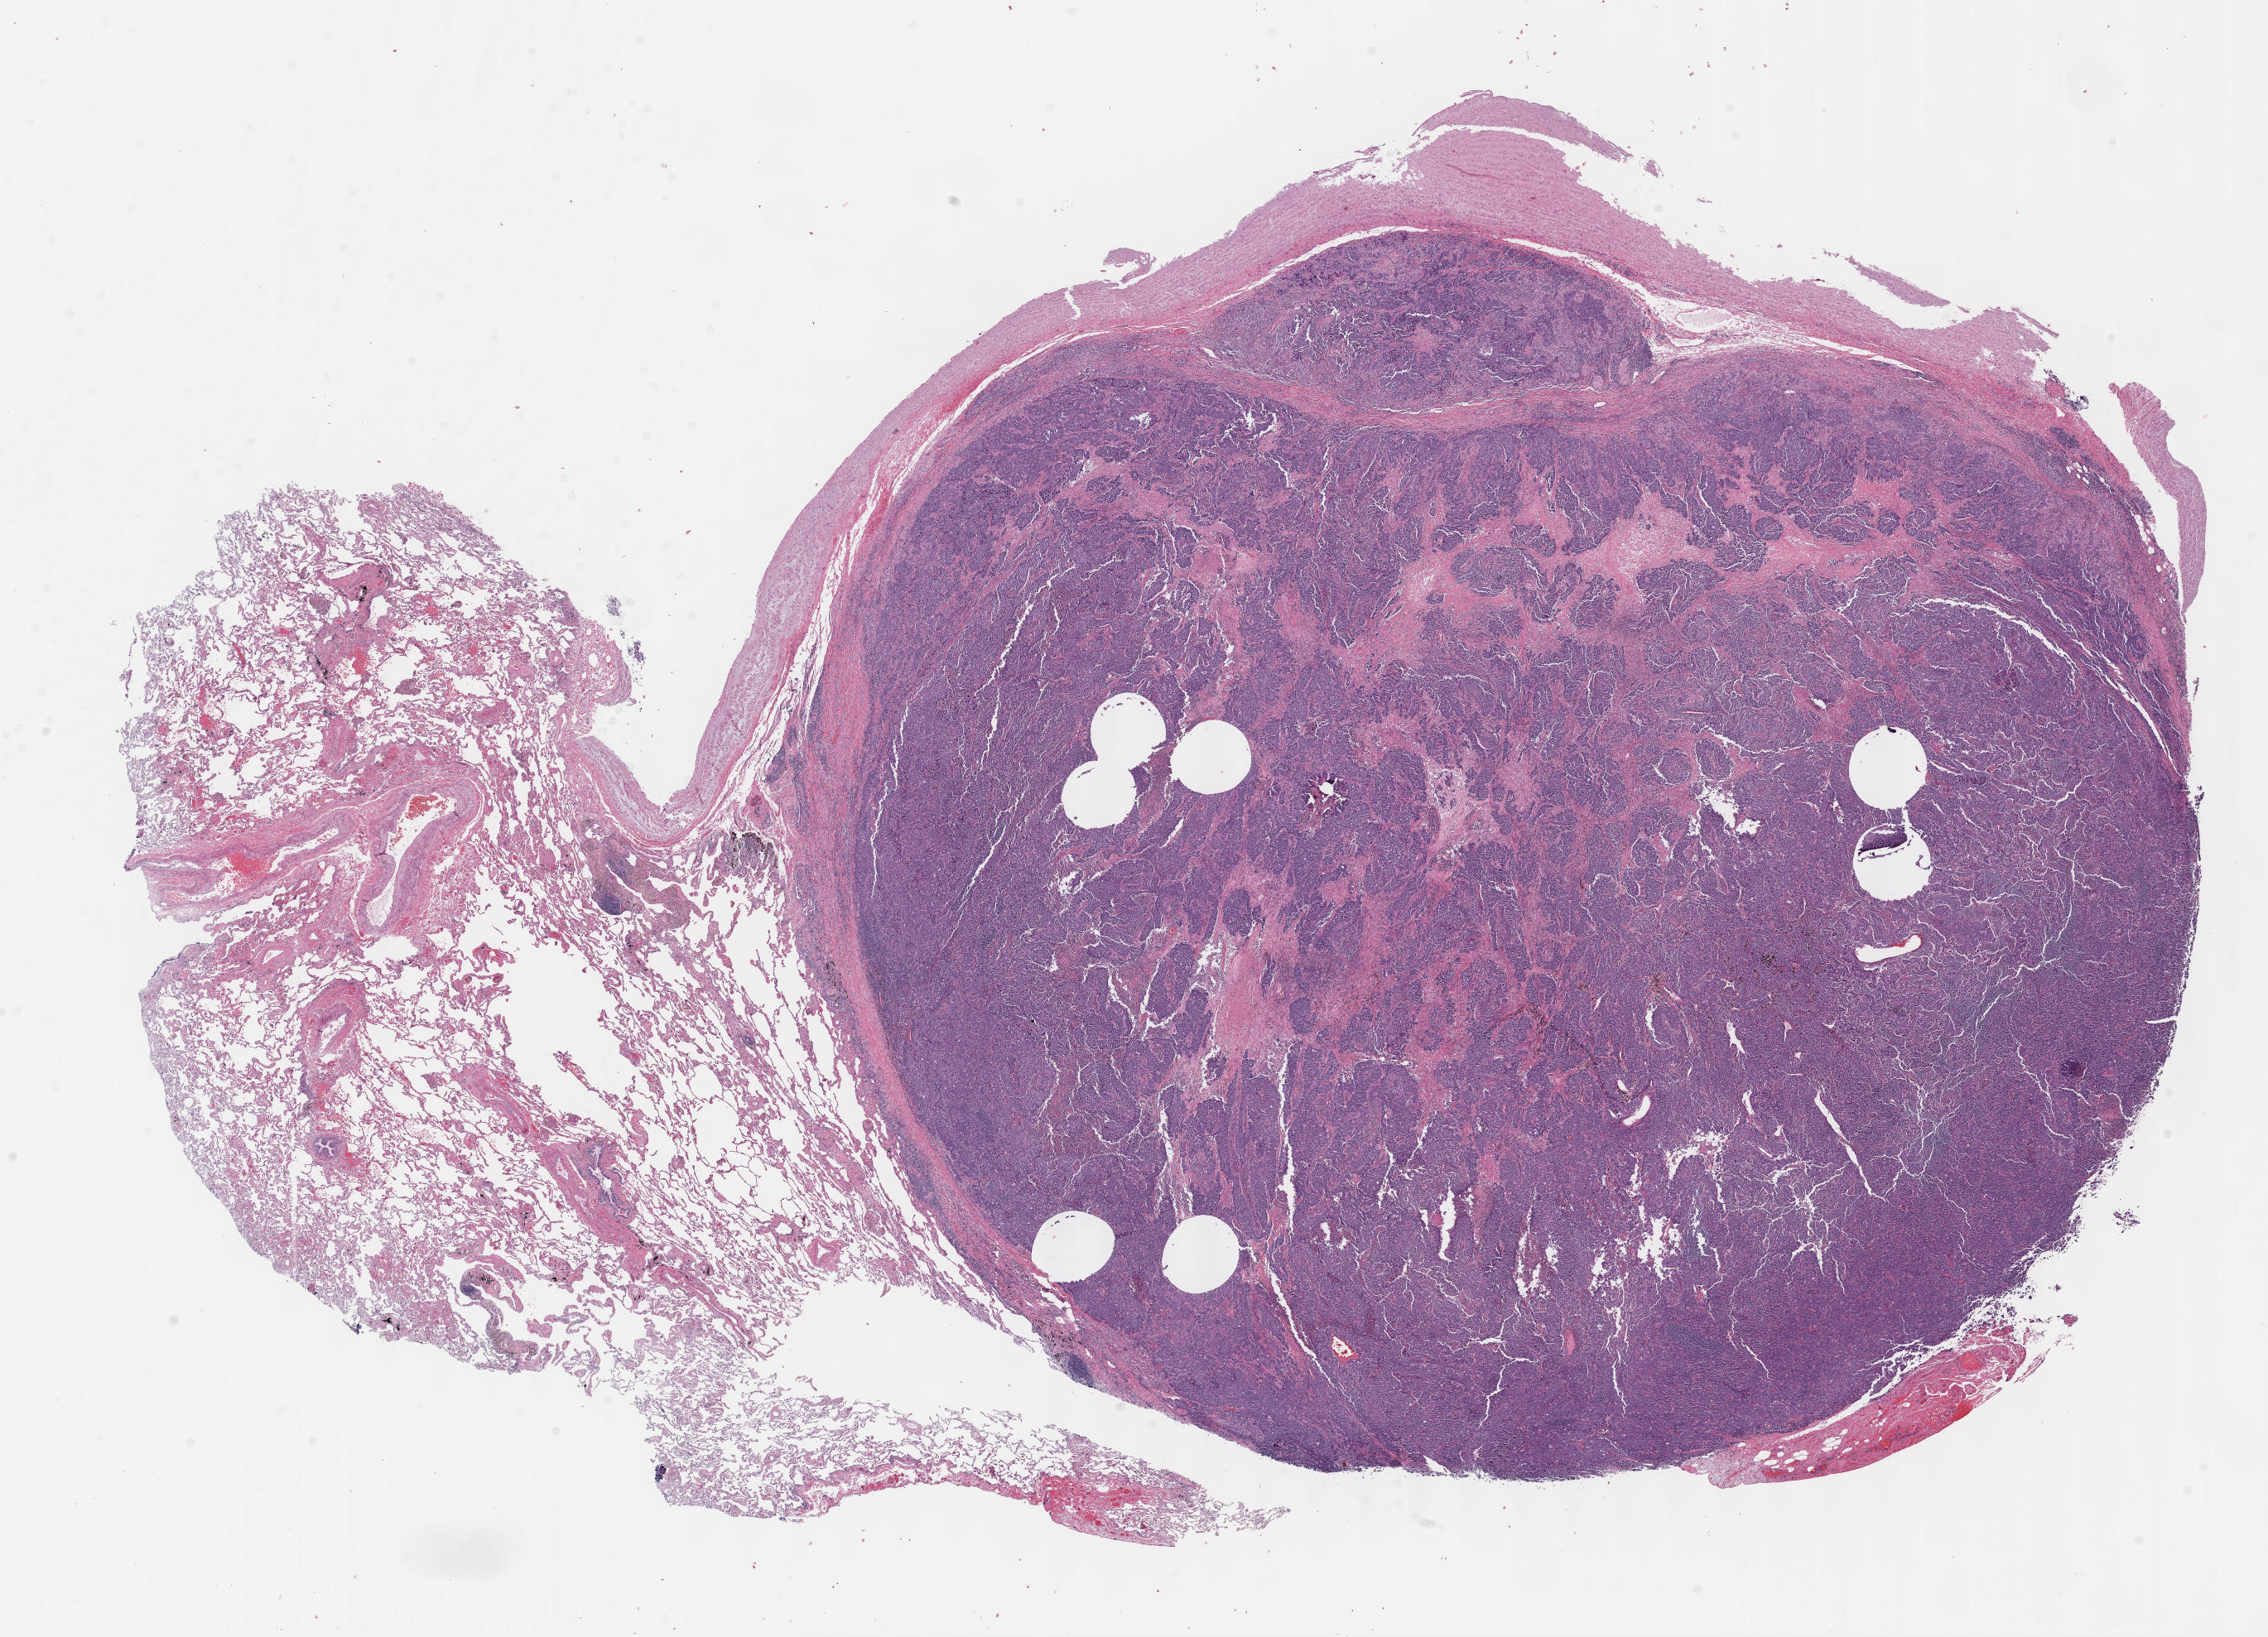
H&E-stained whole-slide image, whole scanned area (about 22.1 x 16.0 mm, acquisition: 40x scan) shown as a low-resolution overview, formalin-fixed paraffin-embedded (FFPE) diagnostic section, sample: primary tumour, lung. Female patient; age at initial diagnosis 72 years.
Pathologic diagnosis: Squamous cell carcinoma, NOS (lower lobe, lung).